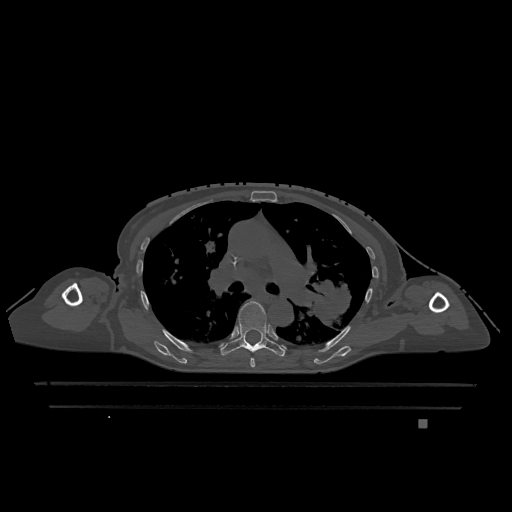
CT including the spine, one axial slice. Position 800 of 1317 along the scan axis. Bone window (W 1800 / L 400 HU). 0.5 mm slice thickness. 512 × 512 image matrix, field of view 500 × 500 mm. Female patient, age 74 years. From the clinical record (not read from this slice): primary cancer: lung; vertebrae with lytic lesions (as recorded): T1, T4, T5, T6, L4, L5.
Structures marked on this image (semi-automatic segmentation, software-assisted and operator-edited):
- T5 vertebra: bounding box <250,358,255,368> (left, top, right, bottom; pixels)
- T6 vertebra: <220,301,285,357>